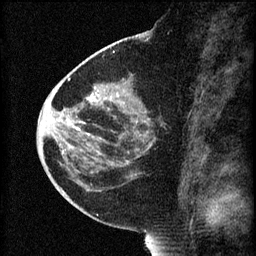
Breast MRI (dynamic contrast-enhanced), one sagittal slice; slice 31 of 60 in the series (ordered by position); 3 images stored at this slice position (order not interpretable as contrast timing); 1.5 T; TE 4.2 ms, TR 8.2 ms; 2 mm slice thickness; 256 × 256 image matrix, field of view 180 × 180 mm. Patient: female, 44 years.
Outlined on this slice (semi-automatic segmentation, software-assisted and operator-edited):
- analysis volume of interest (the breast-tissue region the enhancement analysis was run in; not a lesion): box from (x=73, y=82) to (x=159, y=165) px
- tumour enhancement mask (voxels above the 70 % enhancement threshold inside the analysis volume of interest): (x=74, y=92)–(x=130, y=165)